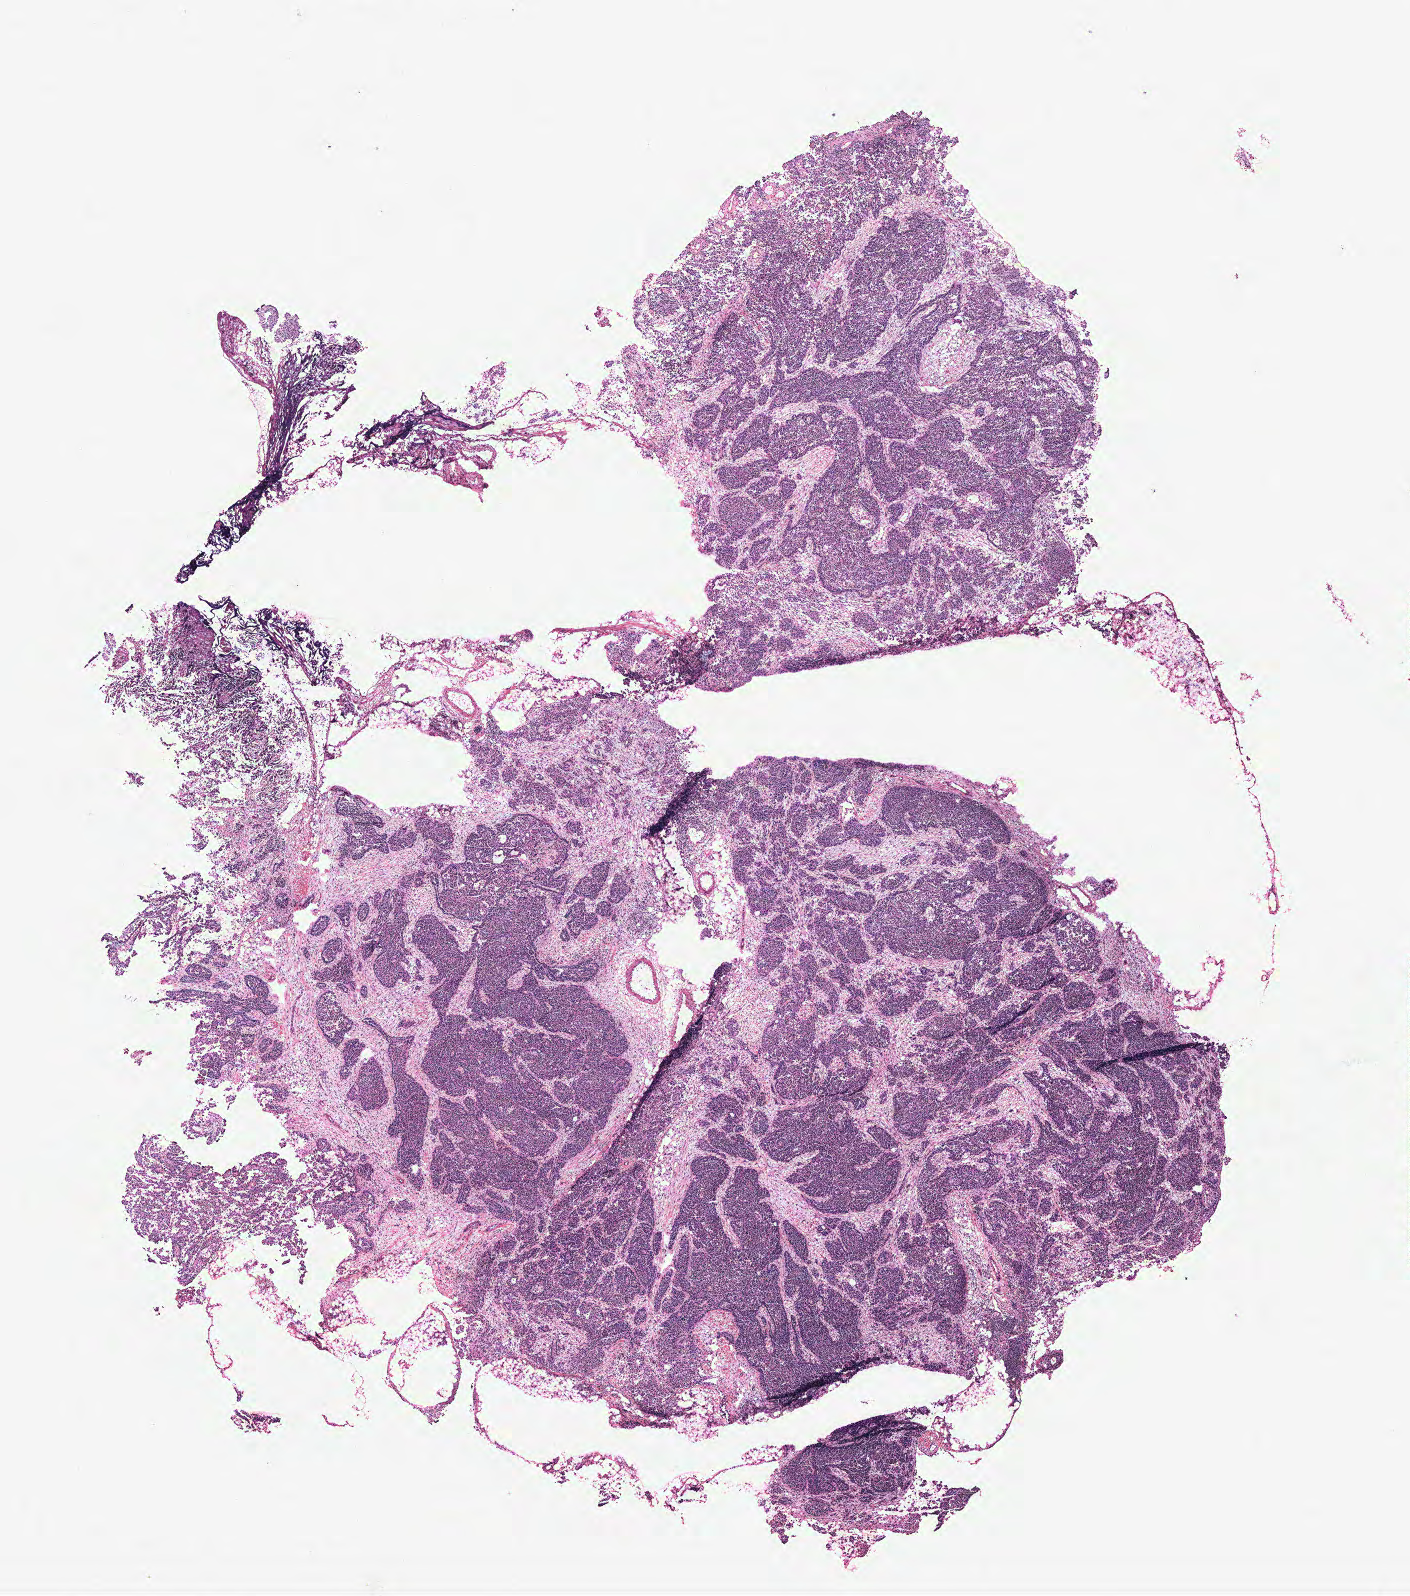
Hematoxylin and eosin (H&E) stained whole-slide image, a low-resolution overview of the entire scanned area, about 11.3 x 12.8 mm. Ovary, tissue type not recorded.
Patient diagnosis (cohort enrolment): ovarian cancer (ovary).